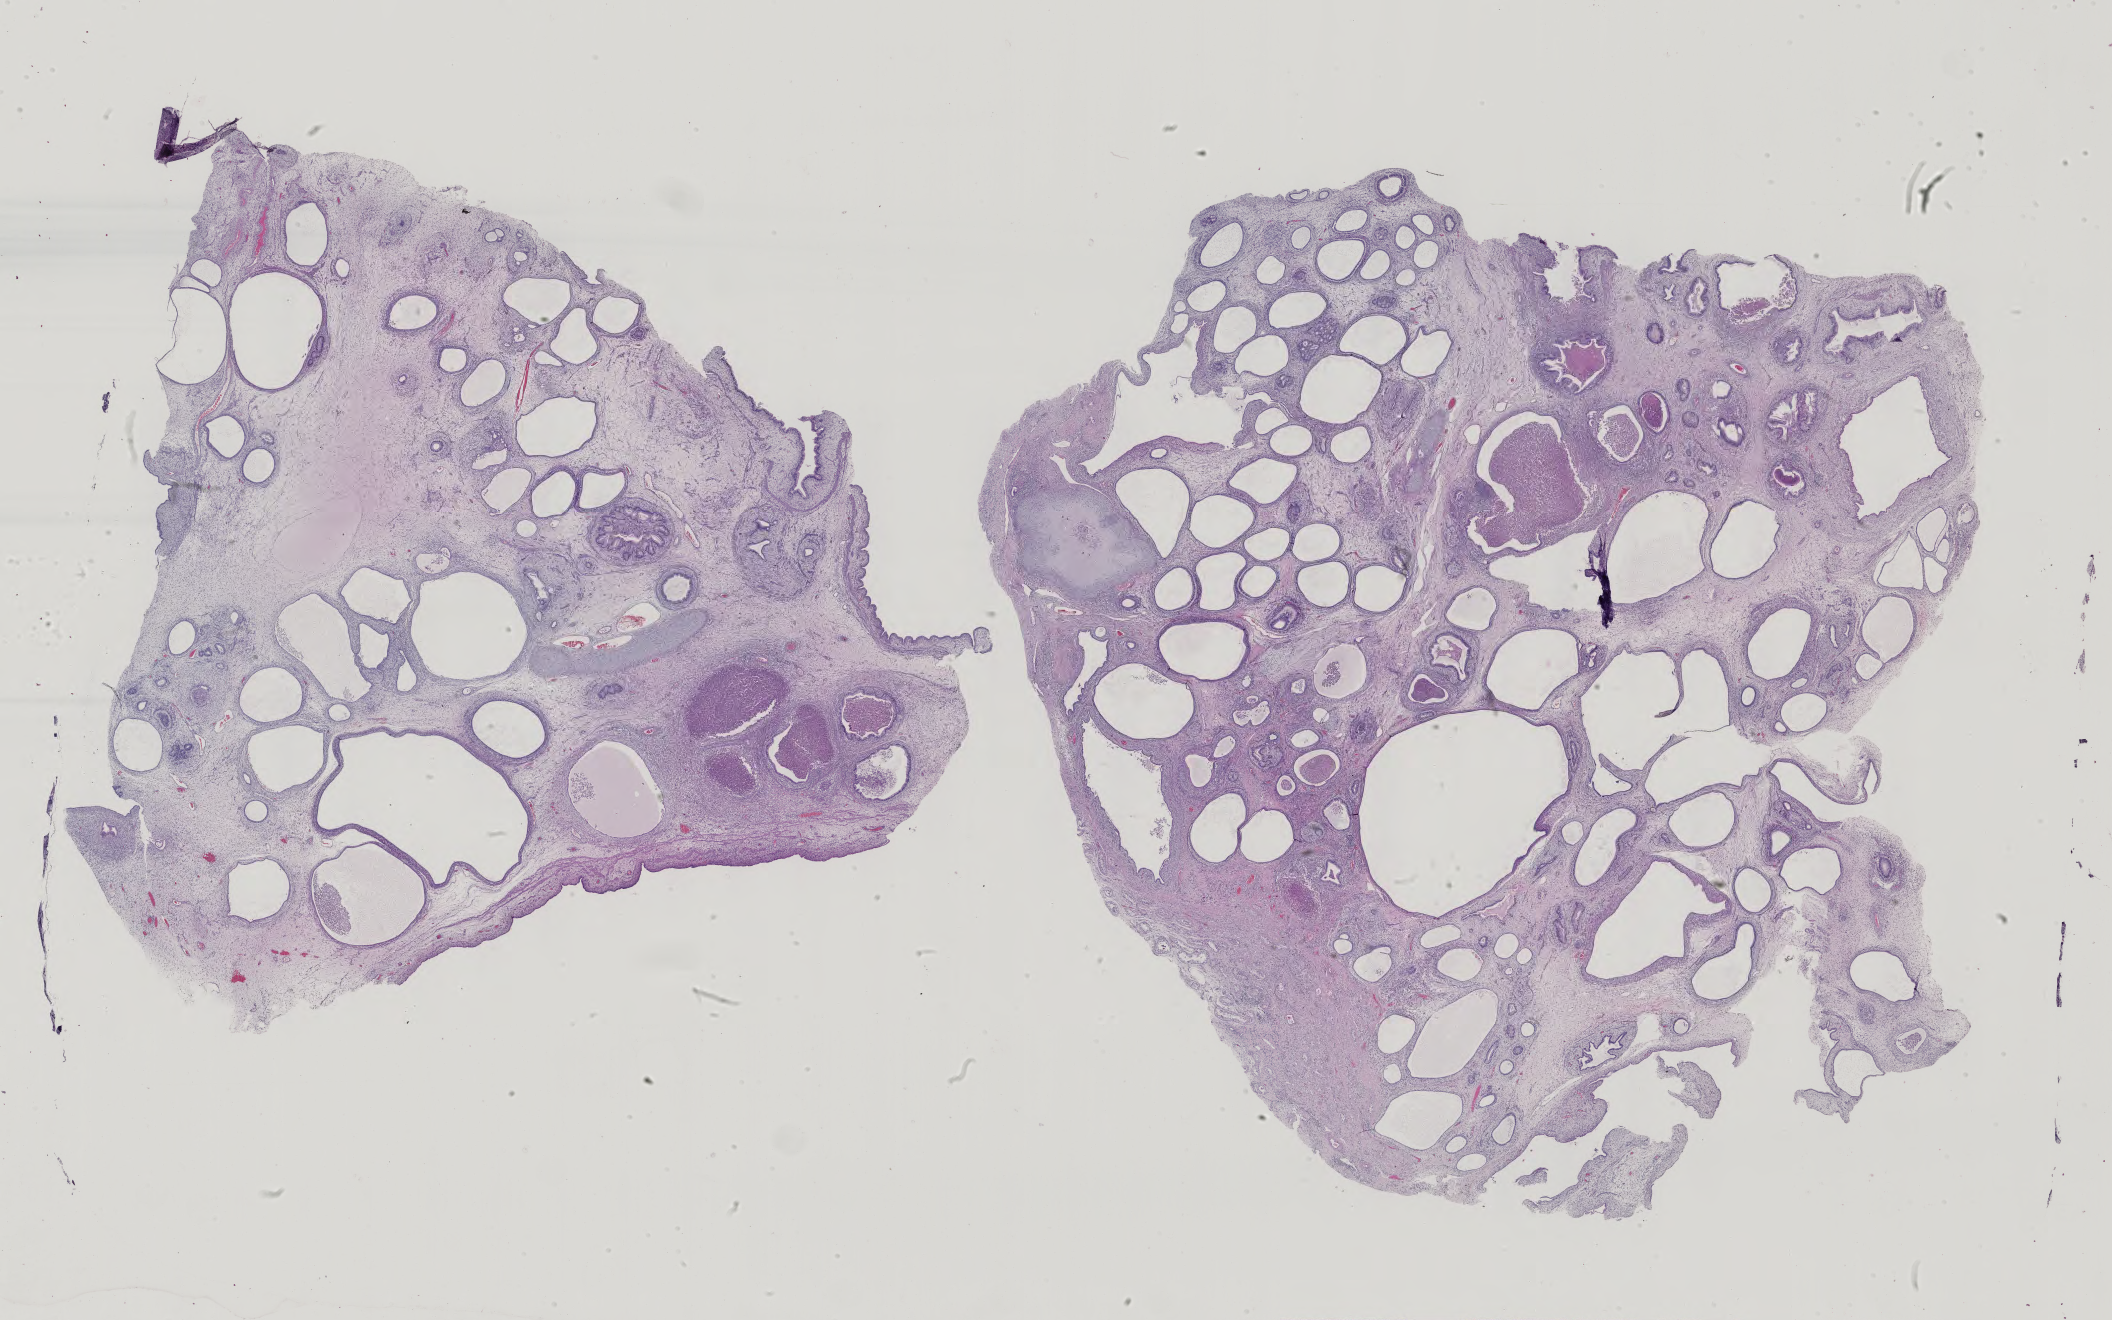
Whole-slide histology image, Hematoxylin and eosin (H&E) stained — whole scanned area (about 30.8 x 19.2 mm) shown as a low-resolution overview. Patient sex: male.
Specimen: FFPE section; testis, primary tumour sample.